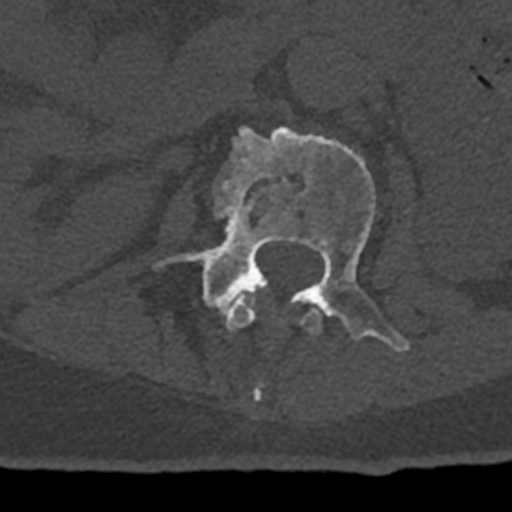
CT including the spine, one axial slice; slice 390 of 797 in the series (ordered by position); reconstruction kernel Br40s/3; bone window (W 1800 / L 400 HU); 0.5 mm slice thickness; 512 × 512 image matrix. Male patient, age 74 years. From the clinical record (not read from this slice): primary cancer: renal.
Structures marked on this image (semi-automatic segmentation, software-assisted and operator-edited):
- L1 vertebra: bounding box (x1, y1, x2, y2) in pixels: (226, 289, 322, 335)
- L2 vertebra: (156, 126, 411, 400)